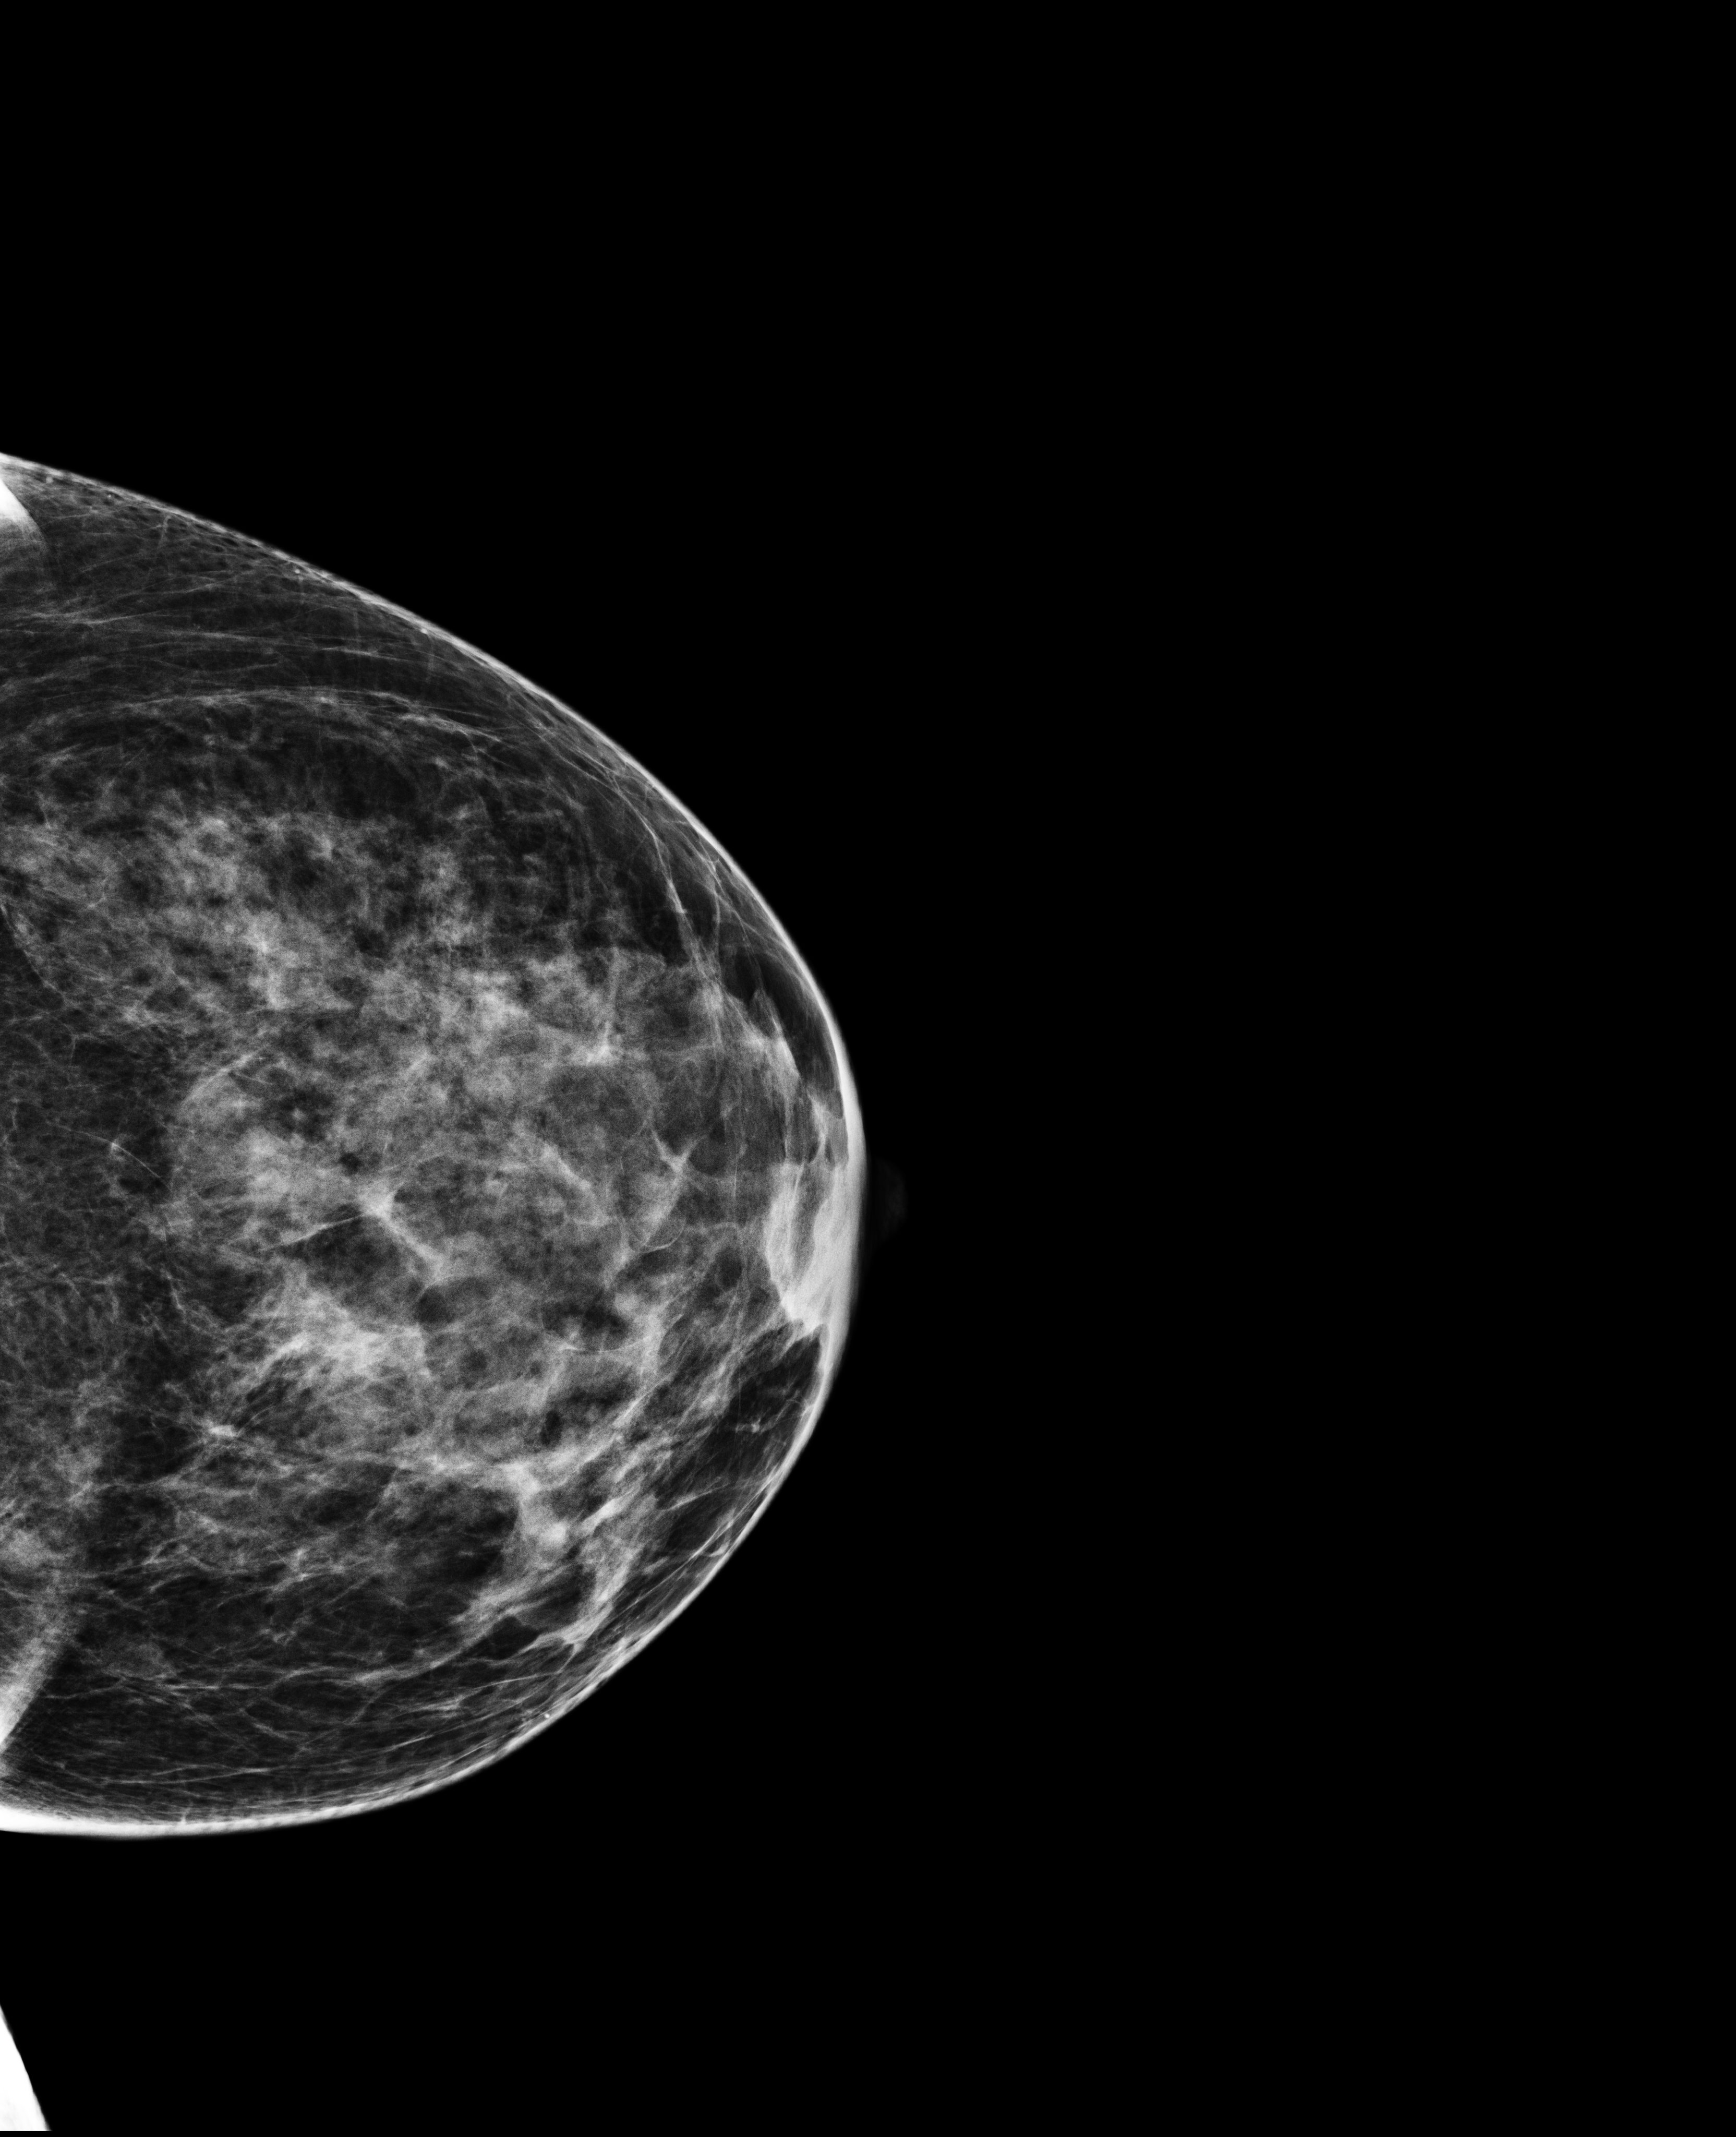
Screening examination, compressed breast thickness 52 mm.
Image type: full-field digital mammogram. Breast: left. Projection: CC view.